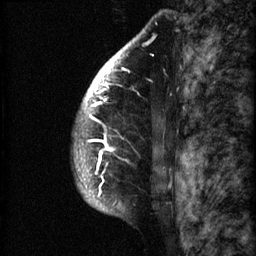
Breast MRI (dynamic contrast-enhanced), one sagittal slice; 3 images stored at this slice position (order not interpretable as contrast timing); 1.5 T; TE 4.2 ms, TR 22.7 ms; 256 × 256 image matrix, field of view 180 × 180 mm. Patient: female, 48 years. Case-level facts recorded for this patient, not image findings: setting: breast cancer imaged before/during neoadjuvant chemotherapy; receptor status: triple-negative.
Outlined on this slice (semi-automatically segmented with operator editing):
- analysis volume of interest (the breast-tissue region the enhancement analysis was run in; not a lesion): bounding box [x1, y1, x2, y2] px = [73, 30, 173, 207]
- tumour enhancement mask (voxels above the 90 % enhancement threshold inside the analysis volume of interest): [76, 38, 140, 206]